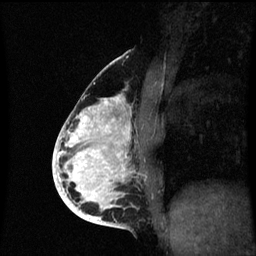
Breast MRI (dynamic contrast-enhanced), one sagittal slice; dynamic contrast-enhanced series, image 2 of 3 at this slice position (ordered by acquisition); 1.5 T; TE 4.2 ms, TR 8.9 ms; 2 mm slice thickness; 256 × 256 image matrix, field of view 200 × 200 mm. Patient: female, 35 years. Case-level facts recorded for this patient, not image findings: setting: breast cancer imaged before/during neoadjuvant chemotherapy; receptor status: HR-positive, HER2-negative.
Outlined on this slice (semi-automatically segmented with operator editing):
- analysis volume of interest (the breast-tissue region the enhancement analysis was run in; not a lesion): bounding box <66,94,144,215> (left, top, right, bottom; pixels)
- tumour enhancement mask (voxels above the 70 % enhancement threshold inside the analysis volume of interest): <66,96,131,215>